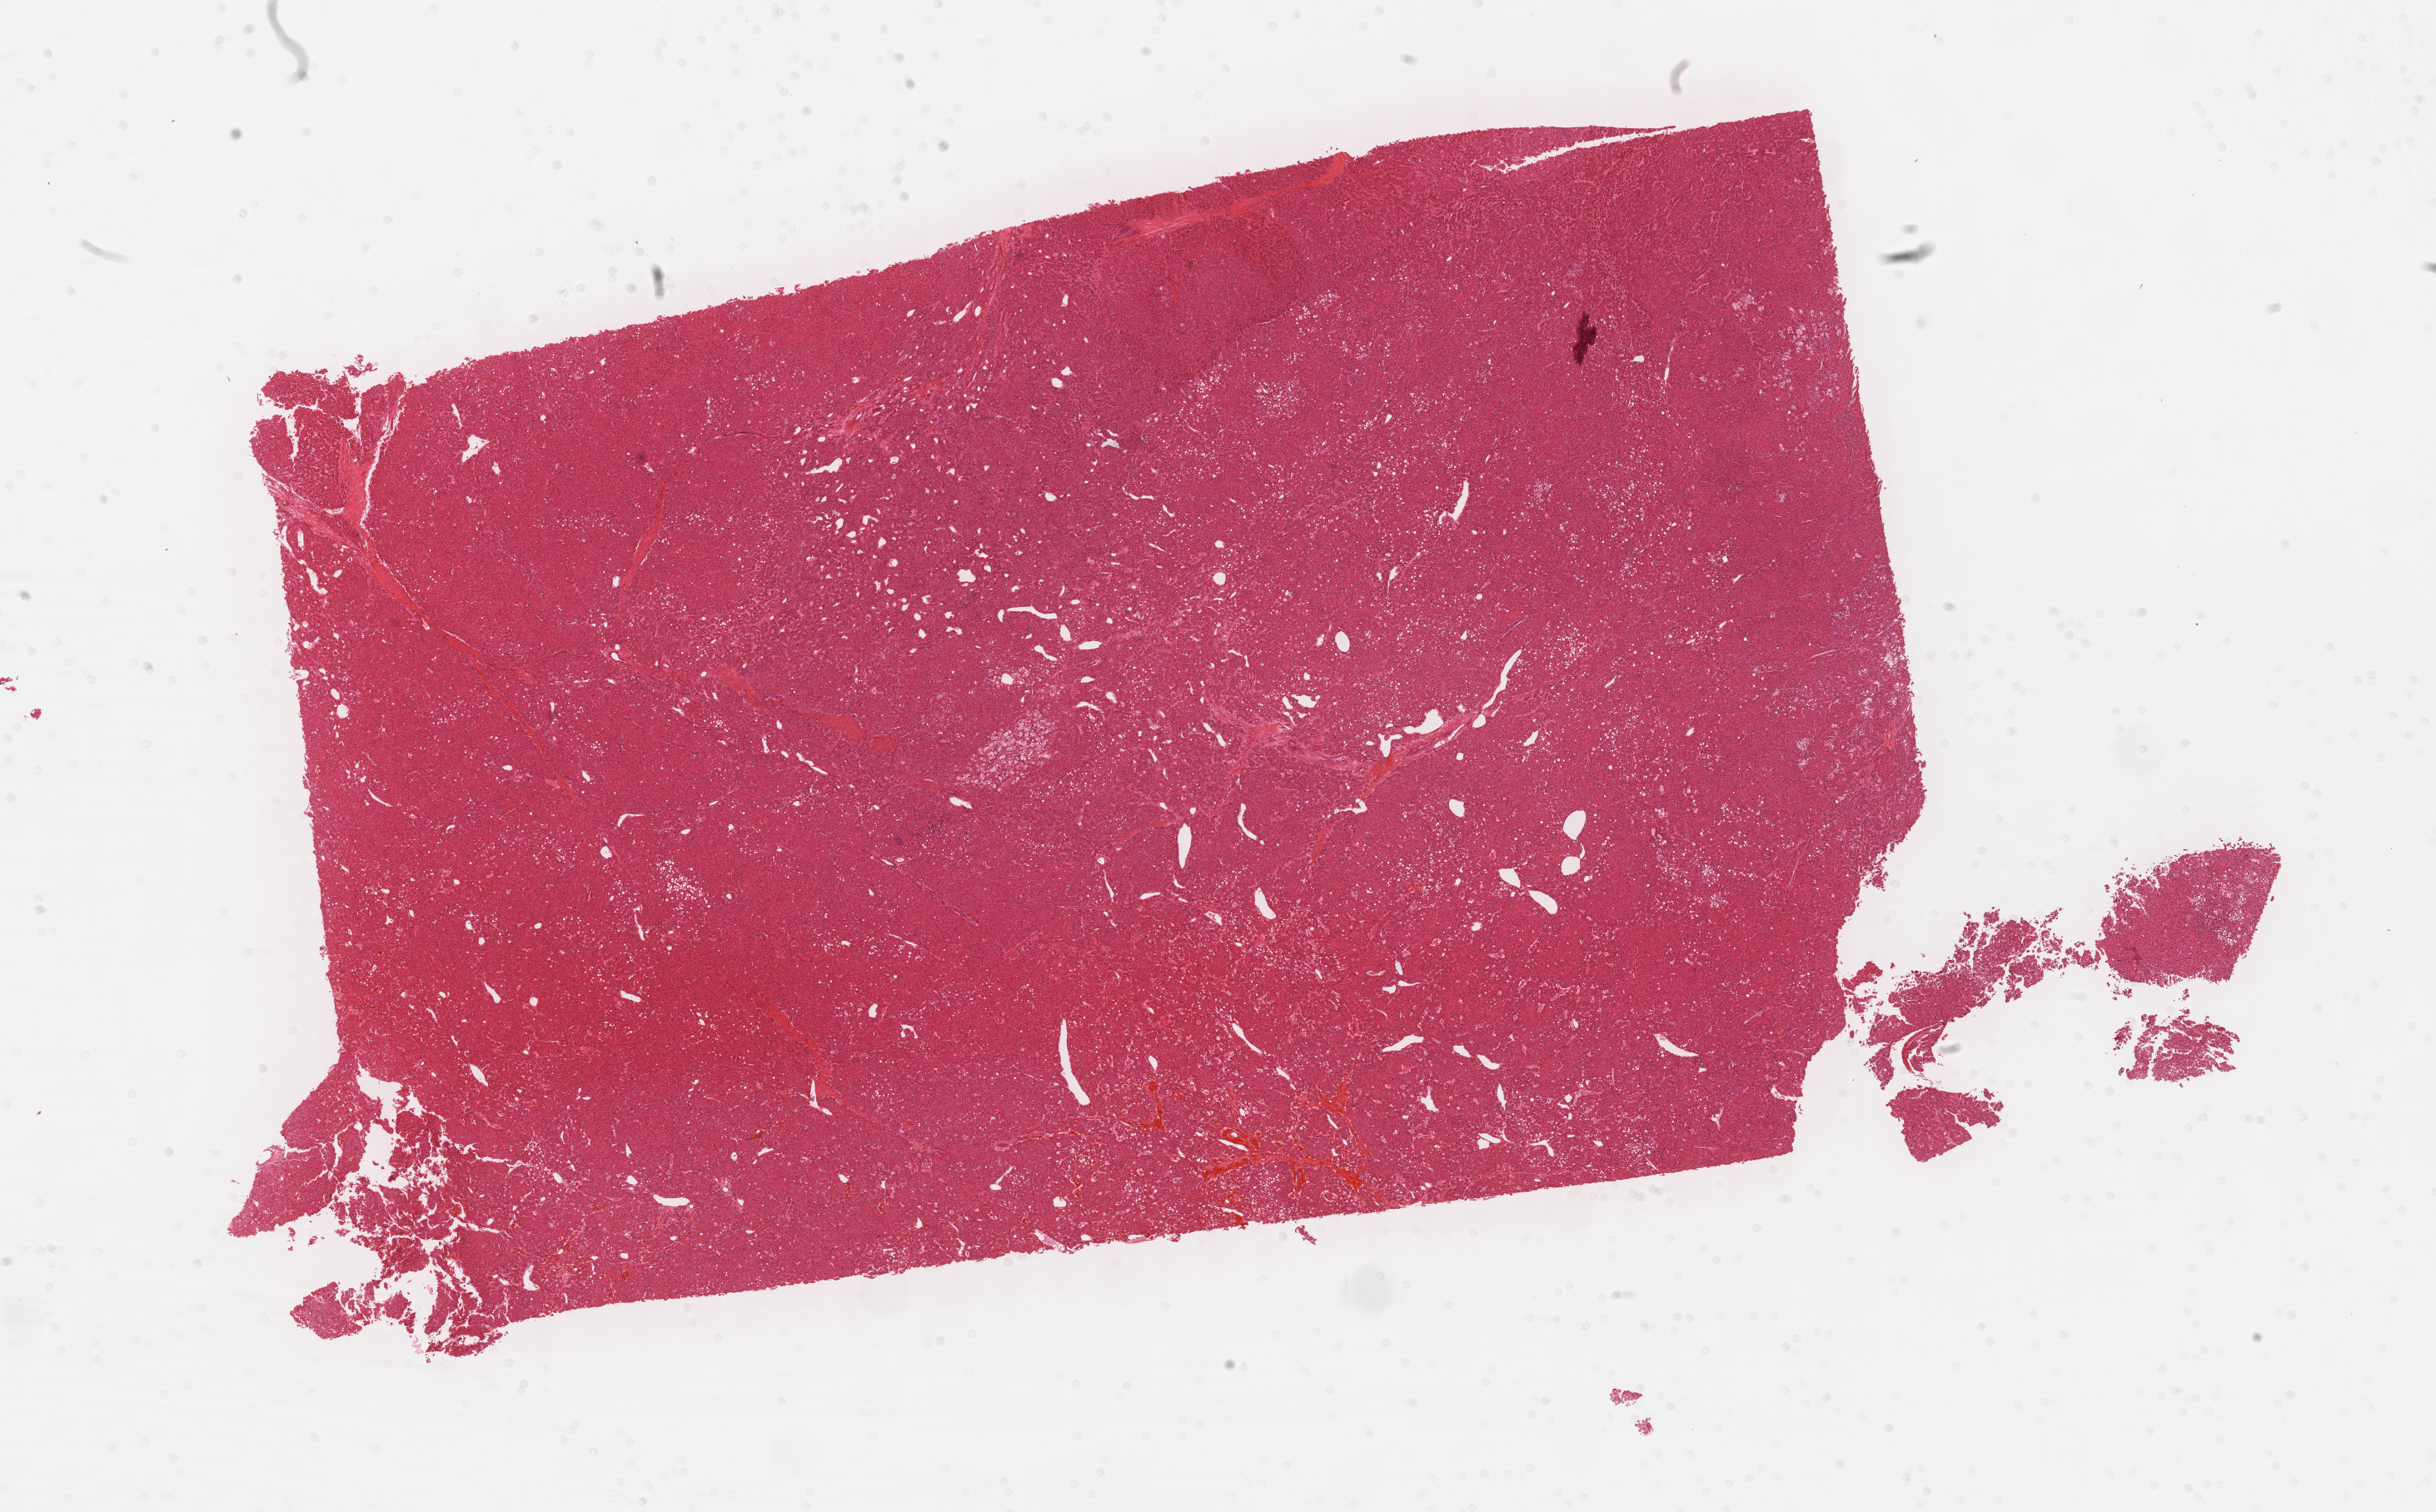
Hematoxylin and eosin (H&E) stained whole-slide image, a low-resolution overview of the entire scanned area, about 23.7 x 14.7 mm; FFPE section; primary tumour sample from the liver. Patient: male, age at initial diagnosis 60 years. Histologic grade: G2 (moderately differentiated).
* AJCC pathologic stage: I
* diagnosis: Hepatocellular carcinoma, NOS